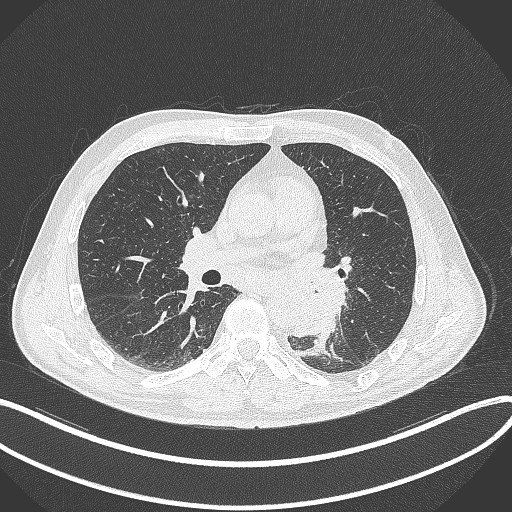
Chest CT, one axial slice. Slice 177 of 329 in the series (ordered by position). Reconstruction kernel B70f. Lung window (W 1500 / L -600 HU). 1 mm slice thickness. 512 × 512 image matrix, field of view 400 × 400 mm. Male patient, age 59 years. From the clinical record (not read from this slice): clinical TNM (as recorded): T2a N2 M0.
Structures marked on this image (rectangle marked by the reading radiologist):
- lung tumour (recorded histology: squamous cell carcinoma): bounding box <282,262,348,341> (left, top, right, bottom; pixels)